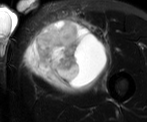
MRI of an extremity soft-tissue mass, one axial slice. Position 40 of 52 along the scan axis. T2-weighted fat-saturated. MR volume resampled by the dataset authors to the PET/CT grid (not the native acquisition matrix). 147 × 122 image matrix, field of view 144 × 119 mm. Male patient. From the clinical record (not read from this slice): histological type: pleiomorphic liposarcoma; grade: high; site of the primary tumour: left thigh.
Outlined on this slice (expert contour drawn on MRI and transferred to this co-registered scan by the dataset authors):
- gross tumour volume including surrounding oedema: bounding box [x1, y1, x2, y2] px = [27, 18, 110, 88]
- gross tumour volume (mass): [27, 21, 106, 88]